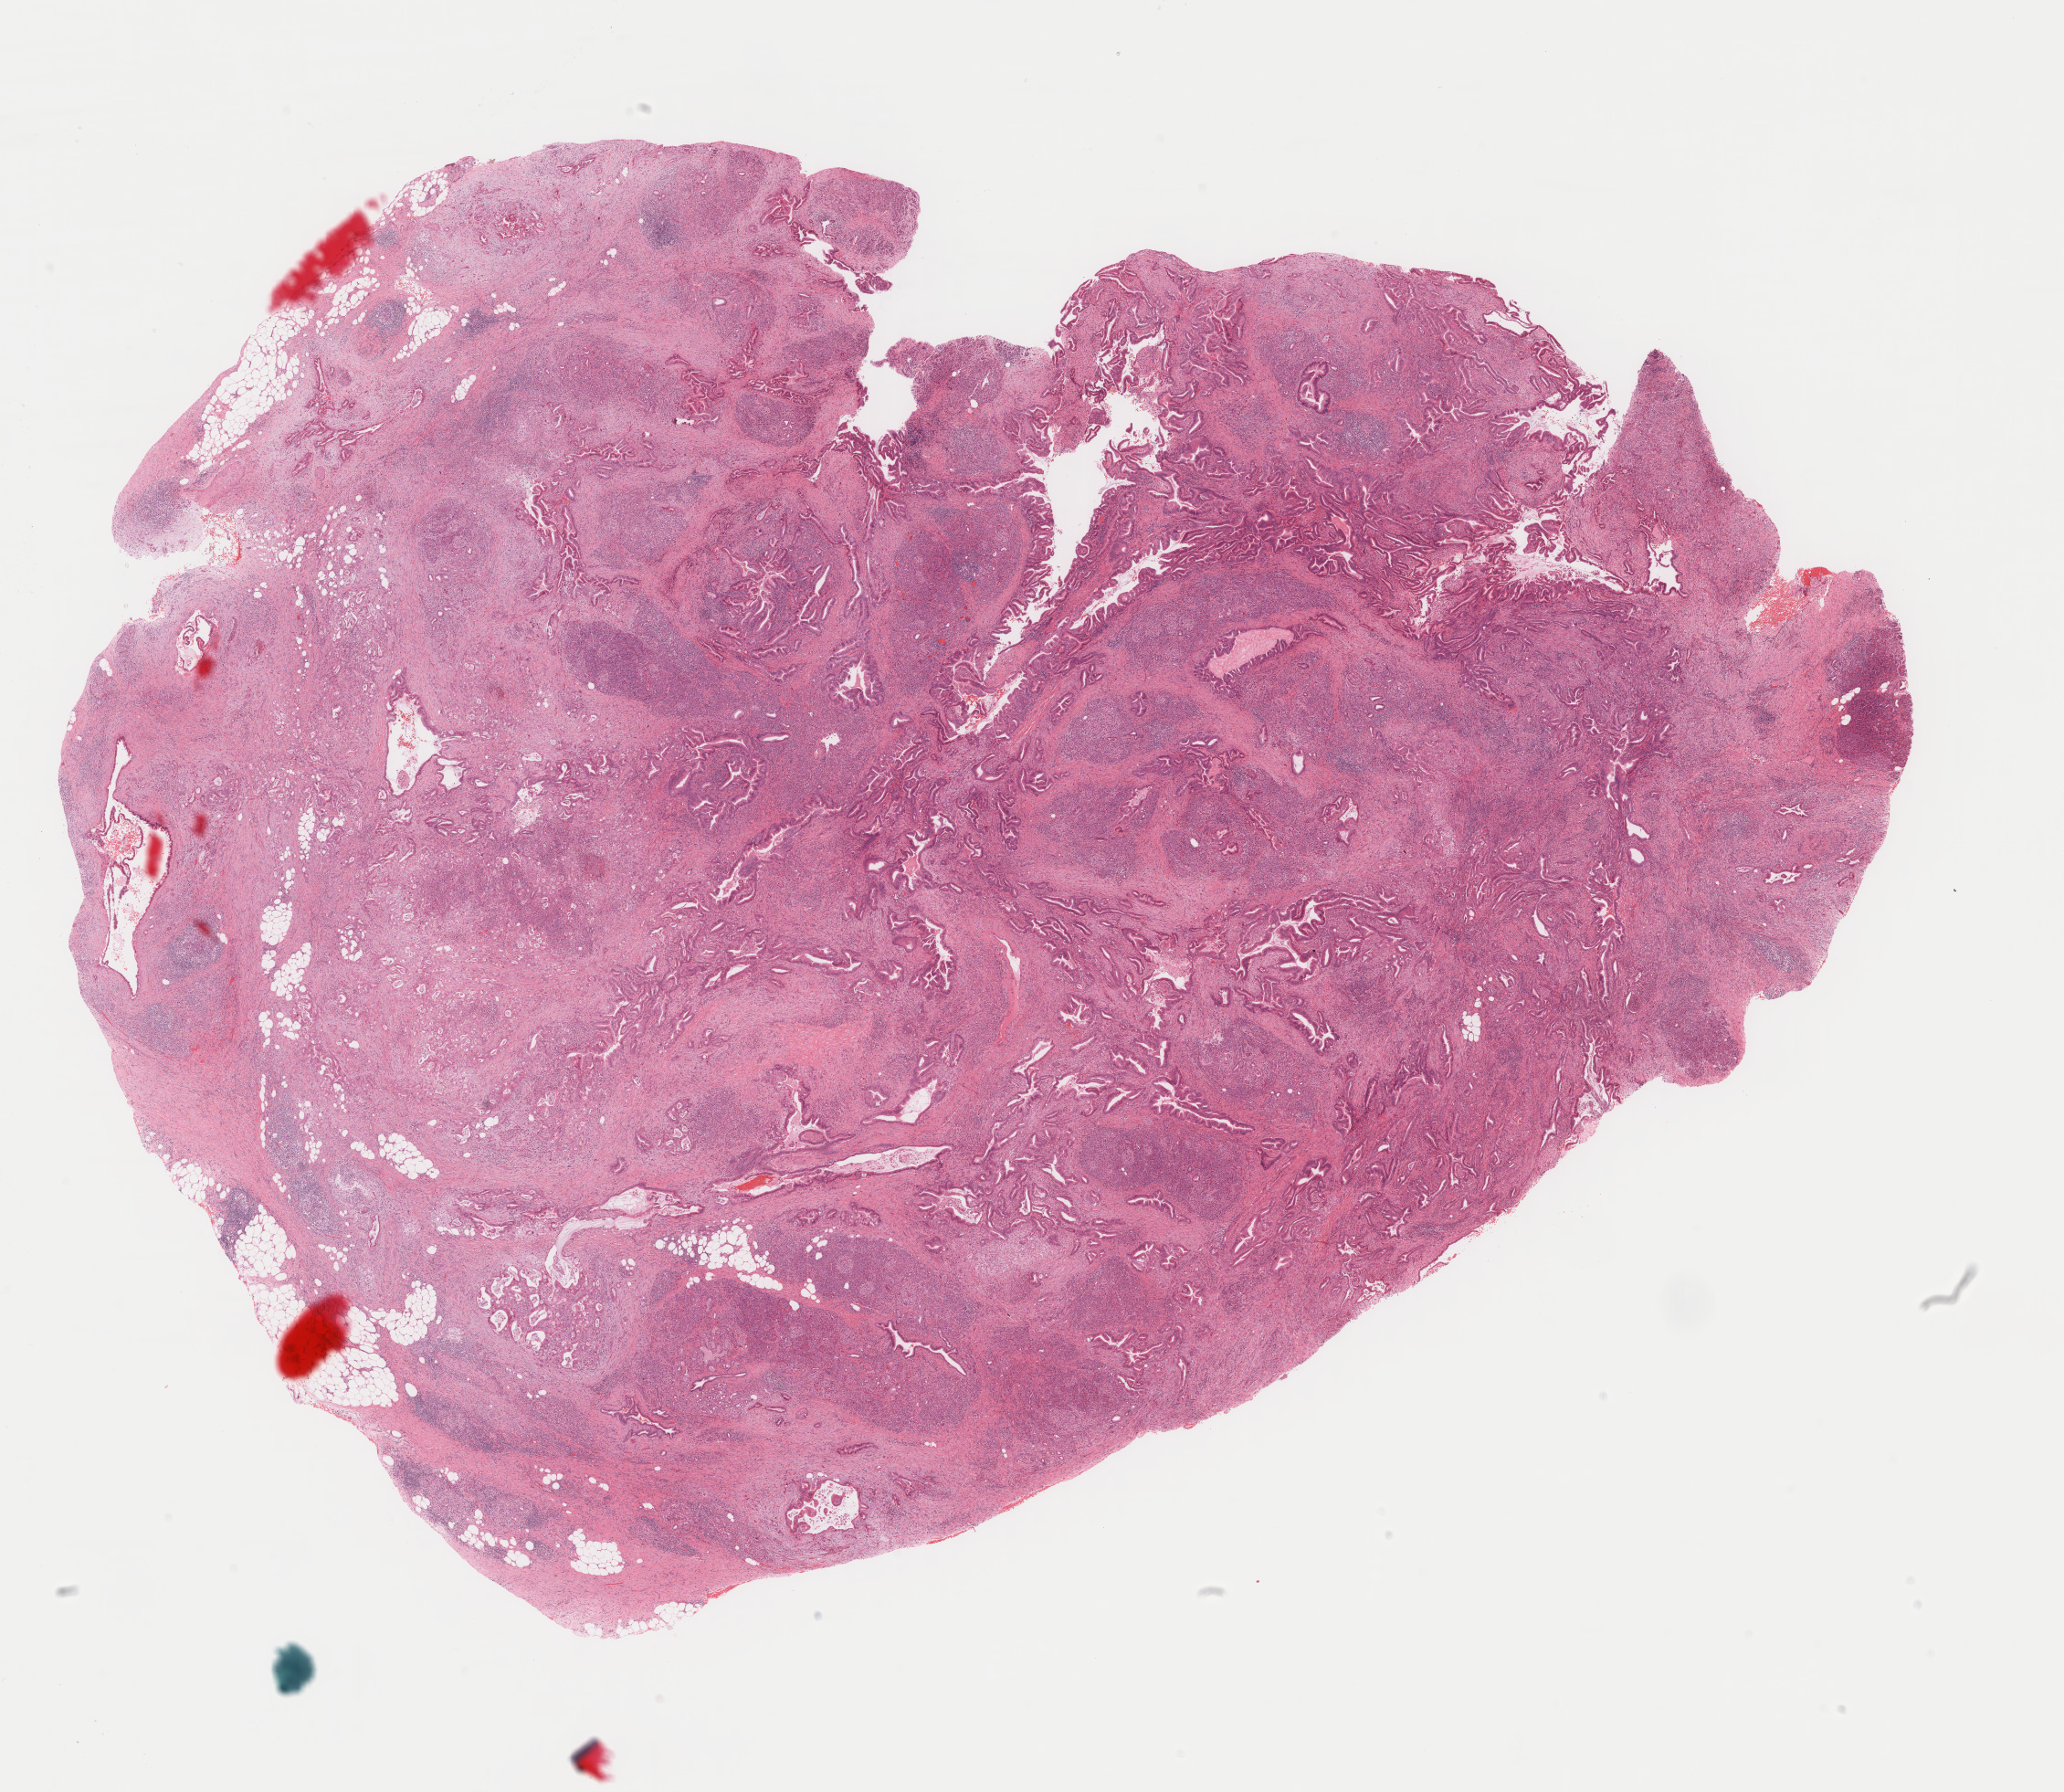
H&E-stained whole-slide image, low-resolution overview of the scanned area, about 17.9 x 15.6 mm (acquisition: 40x scan). Formalin-fixed paraffin-embedded (FFPE) diagnostic section. Pancreas, primary tumour sample. Female, age 69 years at initial diagnosis. Histologic grade: G2 (moderately differentiated).
Pathologic diagnosis: Infiltrating duct carcinoma, NOS (head of pancreas). AJCC pathologic stage: IIB (7th edition).